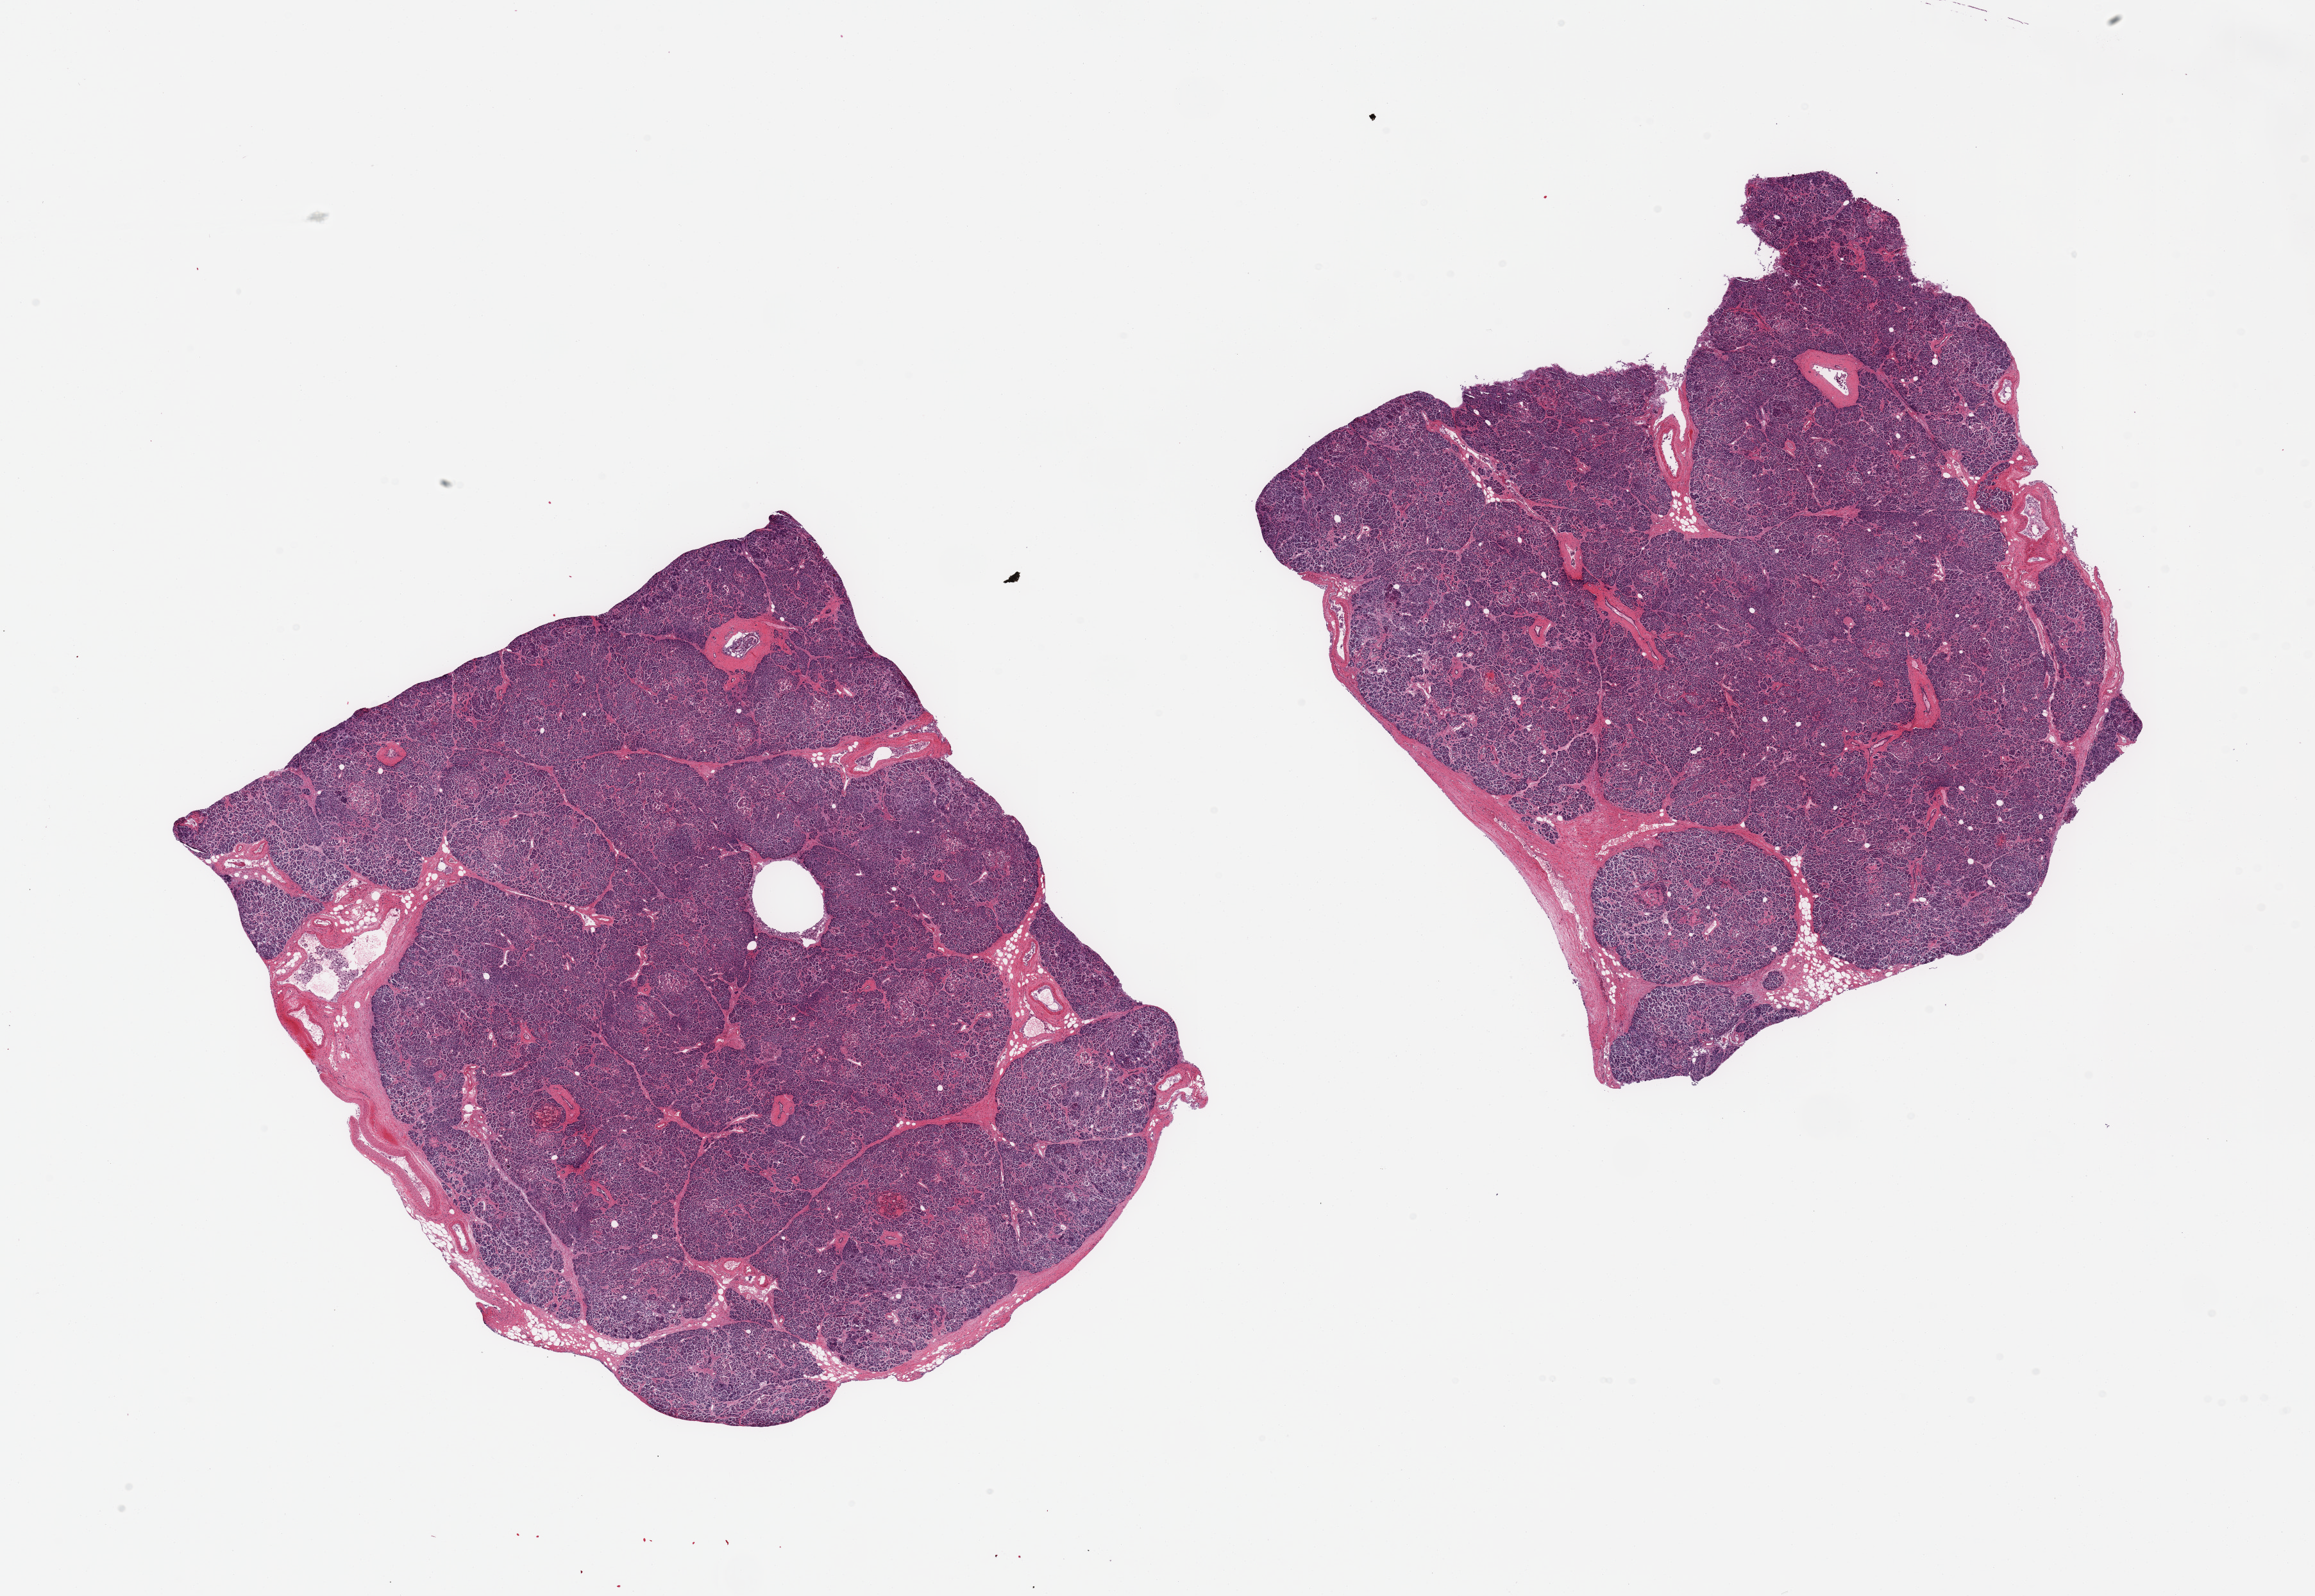
Hematoxylin and eosin (H&E) whole-slide image, whole scanned area (about 28.5 x 19.7 mm) shown as a low-resolution overview. PAXgene-fixed, paraffin-embedded tissue. Sampled site (target tissue): pancreas. Tissue donor sample. Donor: female.
Reviewer comment on this tissue sample: 2 pieces; minimaql internal fat; well trimmed.